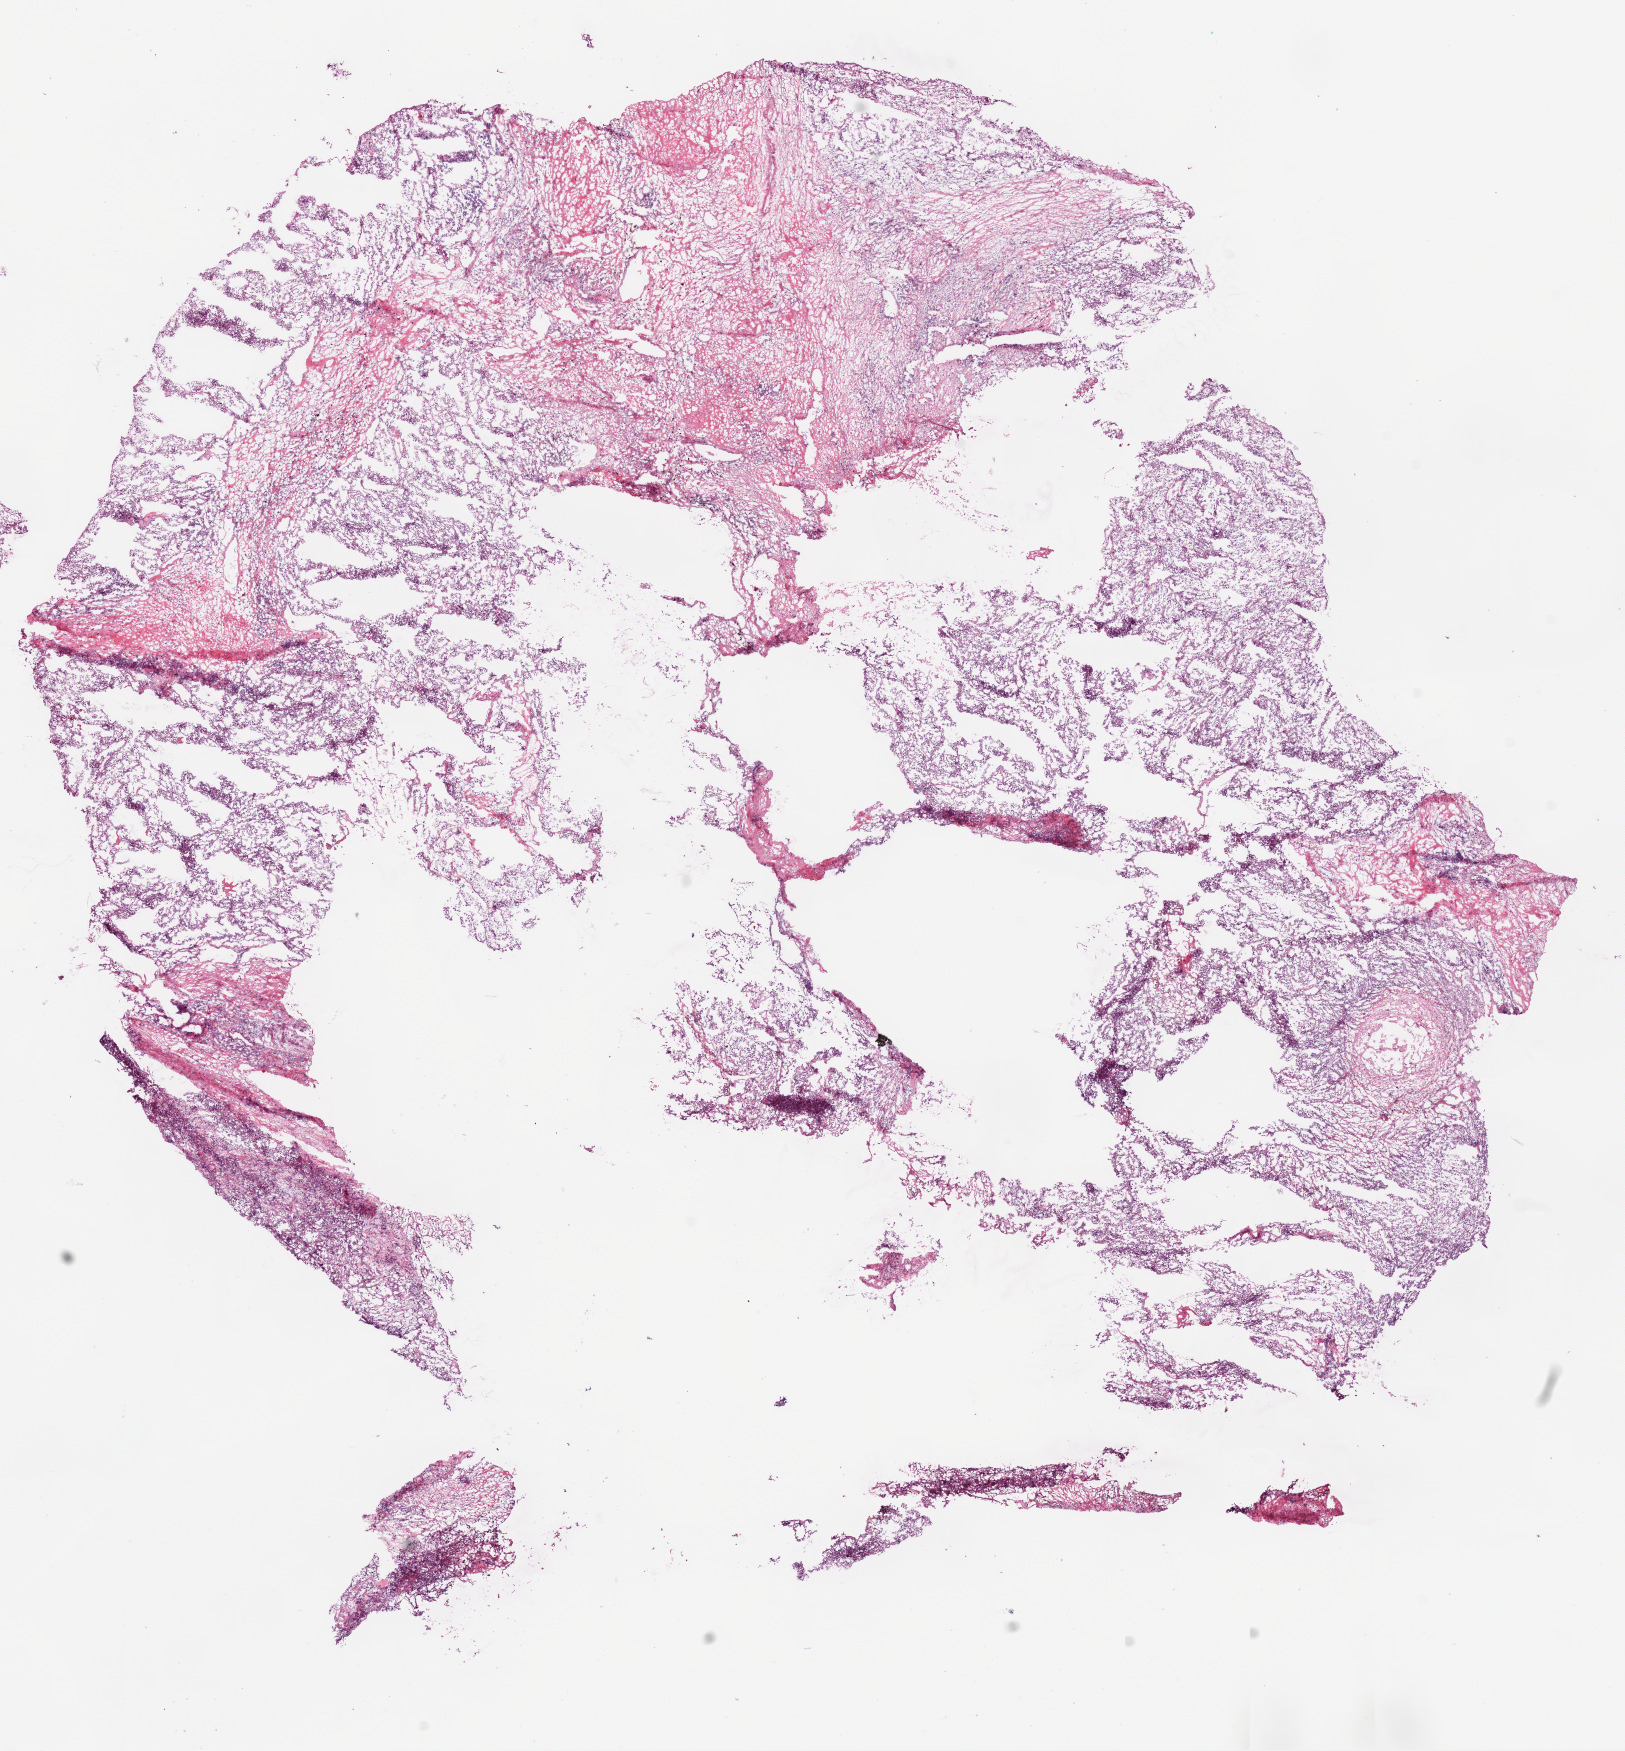
Digitized H&E tissue section (whole slide), a low-resolution overview of the entire scanned area, about 13.0 x 14.1 mm, frozen section from the bottom of the tissue portion, primary tumour sample from the kidney. Male, age 68 years at initial diagnosis.
Histologic diagnosis: Clear cell adenocarcinoma, NOS.